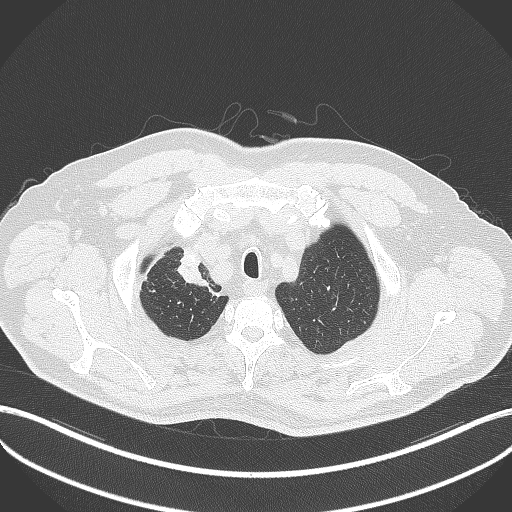
Chest CT, one axial slice. Position 338 of 411 along the scan axis. 120 kVp. Lung window (W 1500 / L -600 HU). 1 mm slice thickness. 512 × 512 image matrix. Patient: male, 60 years. From the clinical record (not read from this slice): clinical TNM (as recorded): T1b N1 M0.
Annotated regions visible in this slice (bounding box drawn by a radiologist):
- lung tumour (recorded histology: squamous cell carcinoma): bounding box (x1, y1, x2, y2) in pixels: (180, 246, 209, 289)